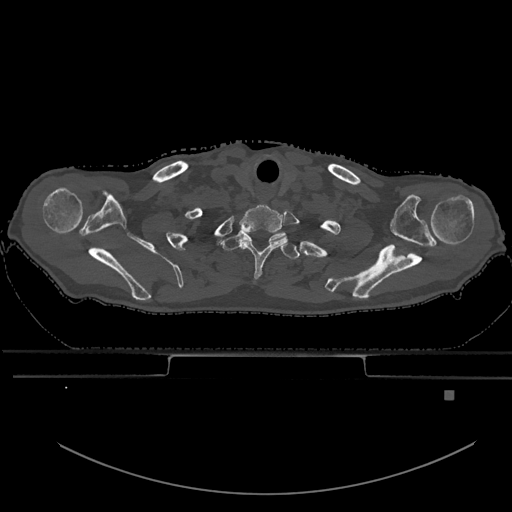
CT including the spine, one axial slice. Bone window (W 1800 / L 400 HU). 0.5 mm slice thickness. 512 × 512 image matrix, field of view 456 × 456 mm. Male patient, age 82 years. Case-level facts recorded for this patient, not image findings: primary cancer: prostate.
Structures marked on this image (semi-automatic segmentation, software-assisted and operator-edited):
- T1 vertebra: bounding box (x1, y1, x2, y2) in pixels: (222, 233, 300, 260)